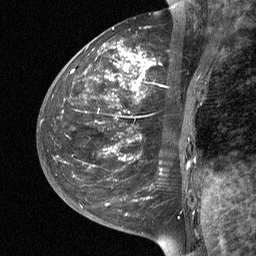
Breast MRI (dynamic contrast-enhanced), one sagittal slice; slice 19 of 64 in the series (ordered by position); dynamic contrast-enhanced study with each time point stored as its own series, time point 2 of 3 at this slice position (early post-contrast, ordered by acquisition time); 1.5 T; TE 4.8 ms, TR 27 ms; 256 × 256 image matrix, field of view 200 × 200 mm. Female patient, age 42 years. Case-level facts recorded for this patient, not image findings: setting: breast cancer imaged before/during neoadjuvant chemotherapy; receptor status: triple-negative.
Annotated regions visible in this slice (semi-automatically segmented with operator editing):
- analysis volume of interest (the breast-tissue region the enhancement analysis was run in; not a lesion): bounding box (x1, y1, x2, y2) in pixels: (43, 29, 203, 190)
- tumour enhancement mask (voxels above the 90 % enhancement threshold inside the analysis volume of interest): (104, 45, 155, 160)